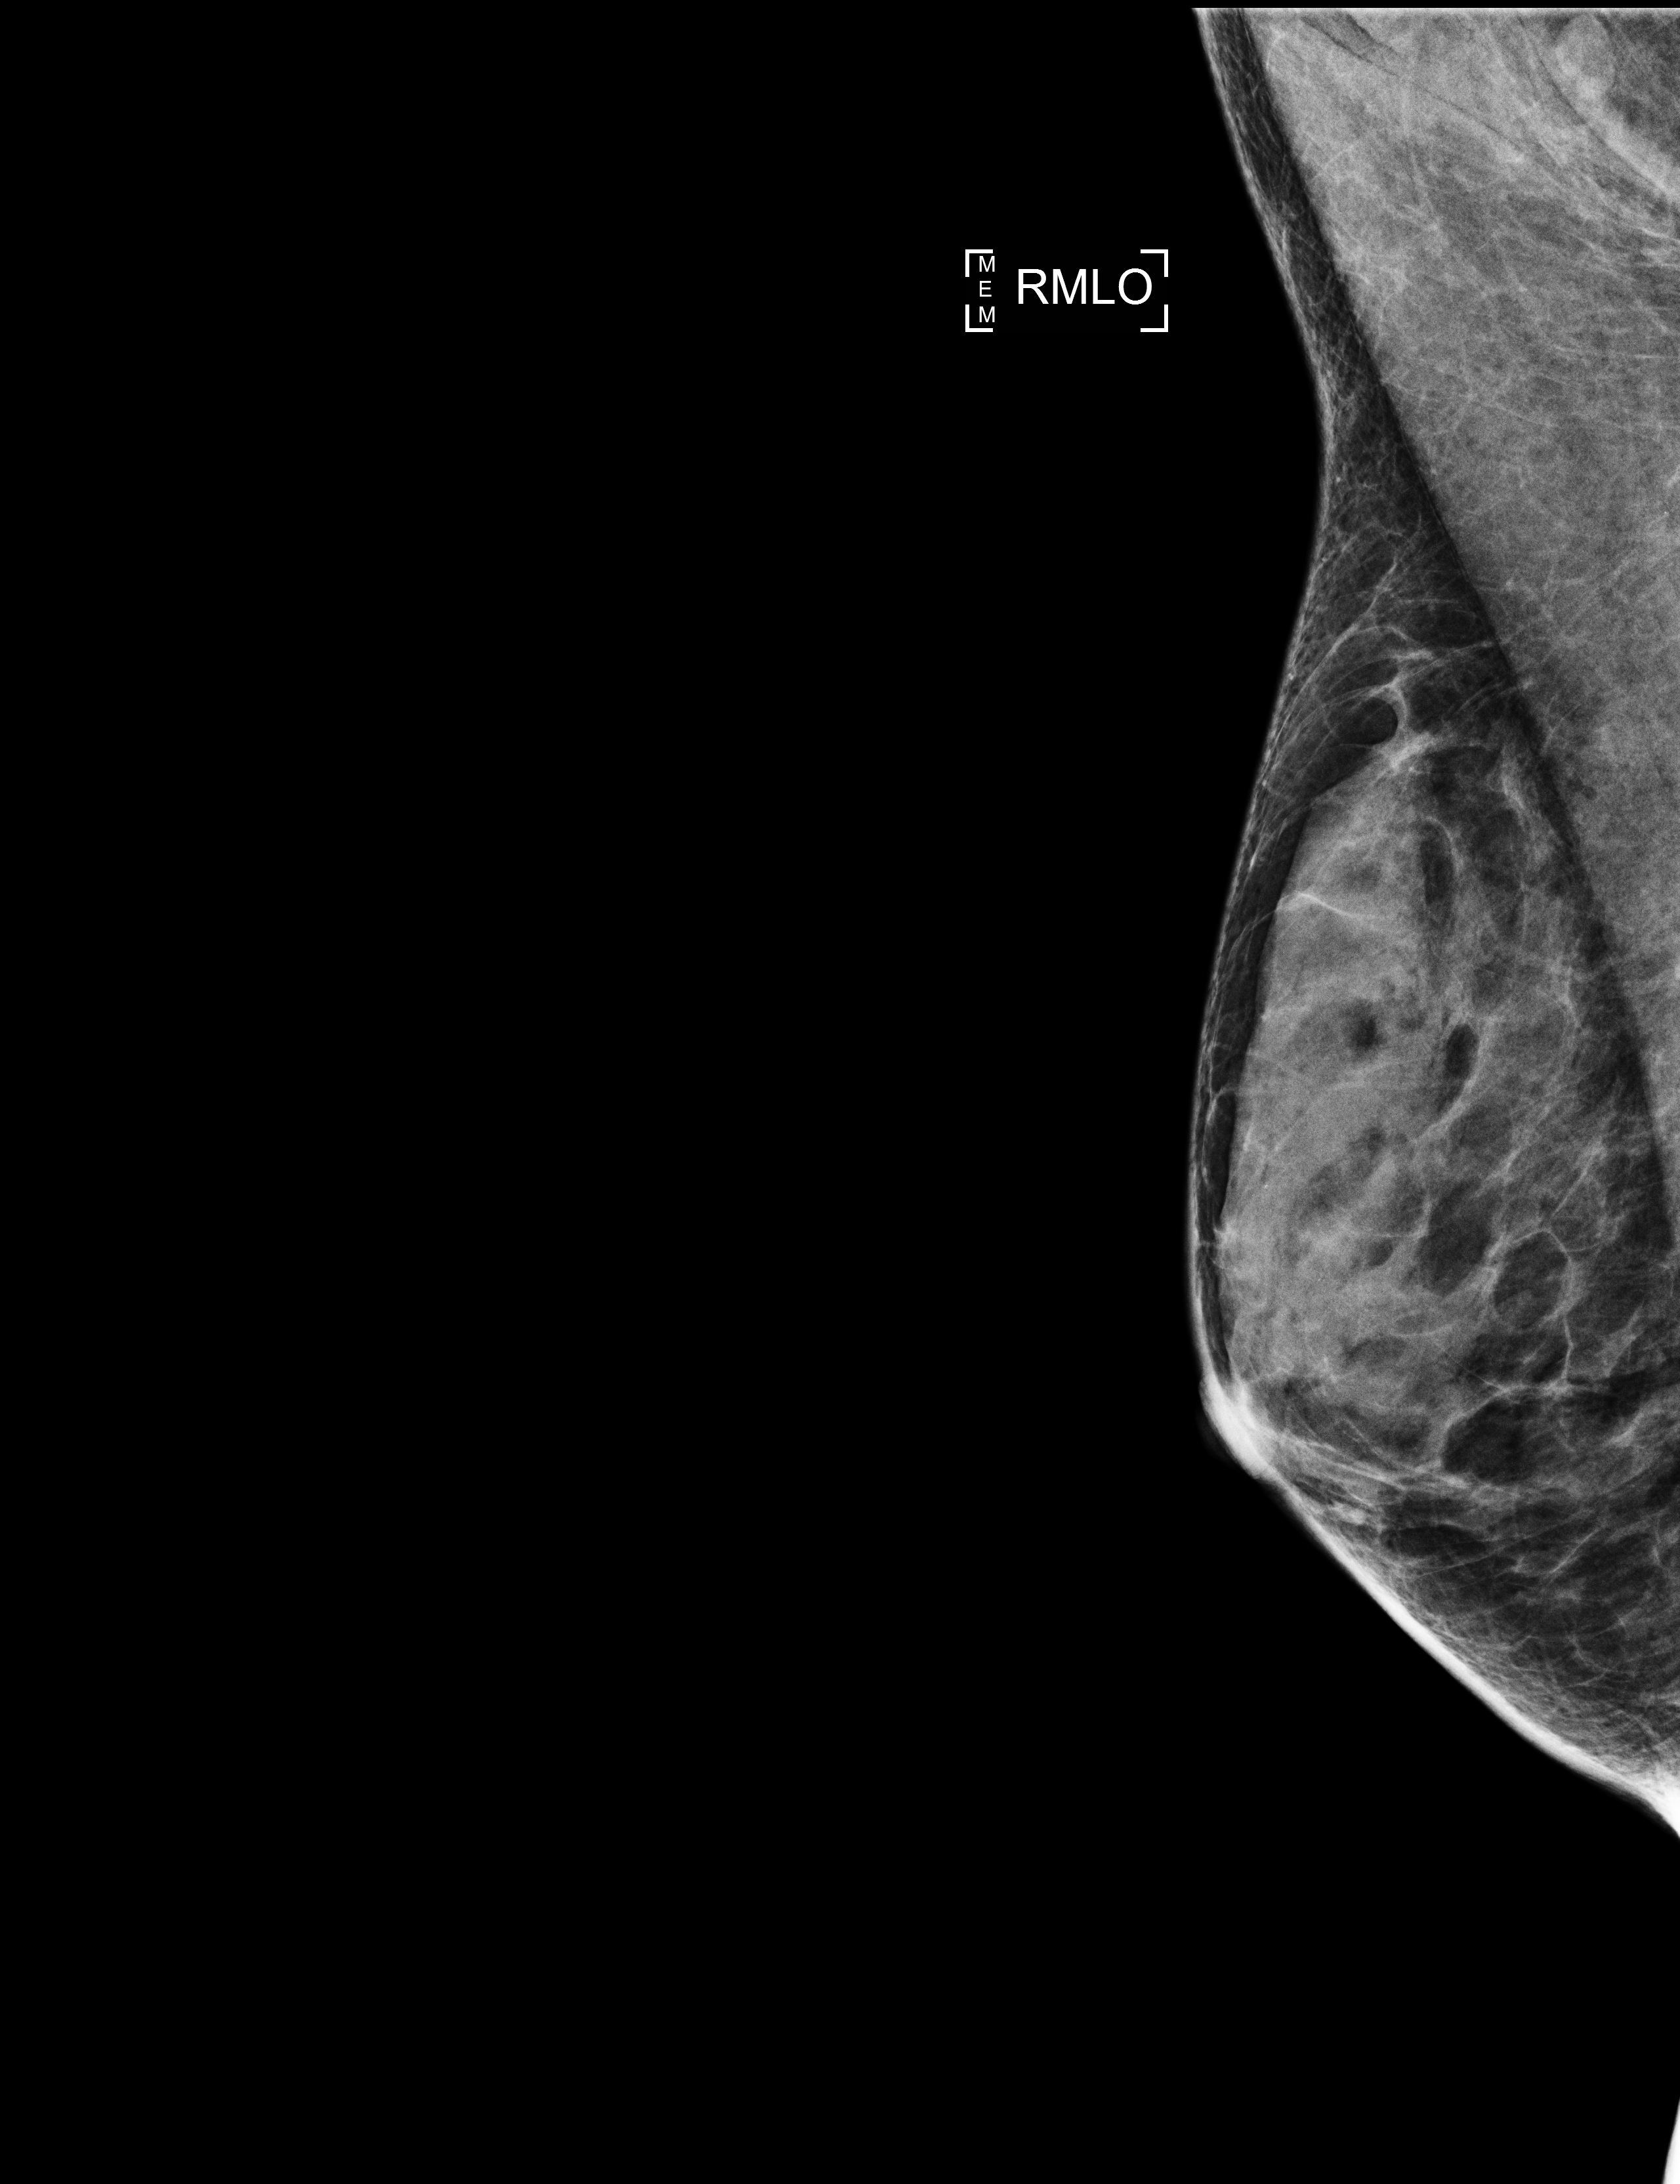
Digital mammogram (FFDM), right breast, MLO view, annual screening mammography examination, system: Selenia Dimensions. Patient aged 60 years (female).
BI-RADS breast density category at the screening exam (both breasts, scale 1–4): 3. Final BI-RADS assessment for this screening round (tomosynthesis exam, both breasts): category 1. Recall: no recall after this screen.